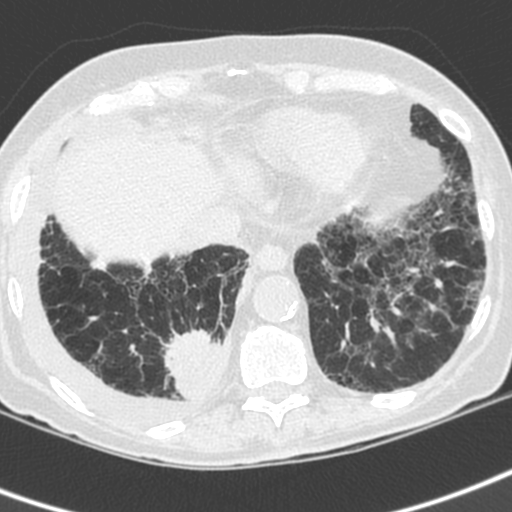
Low-dose screening chest CT, axial slice, first (baseline) screen, lung window (W 1500 / L -600 HU), standard (soft-tissue) reconstruction kernel (C), slice 148 of 192 in the series. Female participant, aged 73 years at enrolment. Current smoker at enrolment.
Expert-annotated lung lesion, bounding box [x1, y1, x2, y2] px = [158, 323, 234, 406]. Reader record for this screening exam (exam-level; its link to the box is not recorded): non-calcified nodule or mass ≥4 mm, right lower lobe, 35 × 30 mm, spiculated (stellate) margins, soft tissue attenuation. Lung cancer was diagnosed 22 days after this screen: adenocarcinoma, NOS, right lower lobe, stage IV (AJCC 6th edition), 35 mm at pathology.